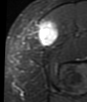
MRI of an extremity soft-tissue mass, one axial slice. Slice 14 of 48 in the series (ordered by position). STIR. MR volume resampled by the dataset authors to the PET/CT grid (not the native acquisition matrix). 87 × 102 image matrix, field of view 85 × 100 mm. Female patient. From the clinical record (not read from this slice): histological type: synovial sarcoma; grade: intermediate; site of the primary tumour: right thigh.
Annotated regions visible in this slice (expert contour drawn on MRI and transferred to this co-registered scan by the dataset authors):
- gross tumour volume including surrounding oedema: box from (x=38, y=20) to (x=59, y=46) px
- gross tumour volume (mass): (x=38, y=20)–(x=59, y=46)